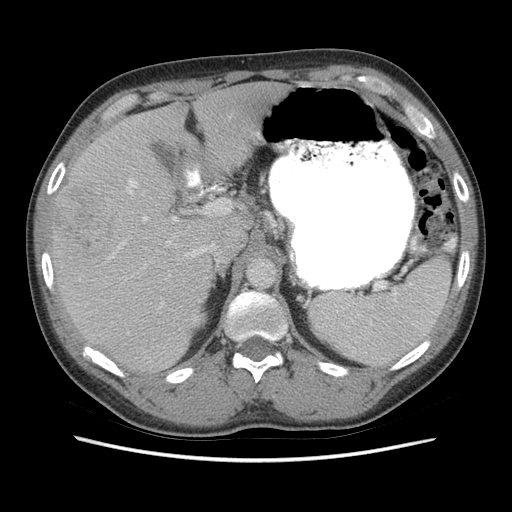
Contrast-enhanced abdominal CT (liver protocol), one axial slice. Position 42 of 73 along the scan axis. Soft-tissue window (W 400 / L 40 HU). 512 × 512 image matrix, field of view 360 × 360 mm. Case-level facts recorded for this patient, not image findings: diagnosis: hepatocellular carcinoma (patient treated with transarterial chemoembolisation; whether this scan precedes or follows treatment is not stated here); TNM stage (as recorded): Stage-IIIA; Child-Pugh class: A; tumour size: 6.6 cm.
Annotated regions visible in this slice (semi-automatic segmentation, software-assisted and operator-edited):
- liver parenchyma outside the tumour (the mass and vessels are separate outlines, so this box may not span the whole liver): bounding box <50,82,288,372> (left, top, right, bottom; pixels)
- mass: <57,188,113,257>
- liver vessels: <108,179,231,308>